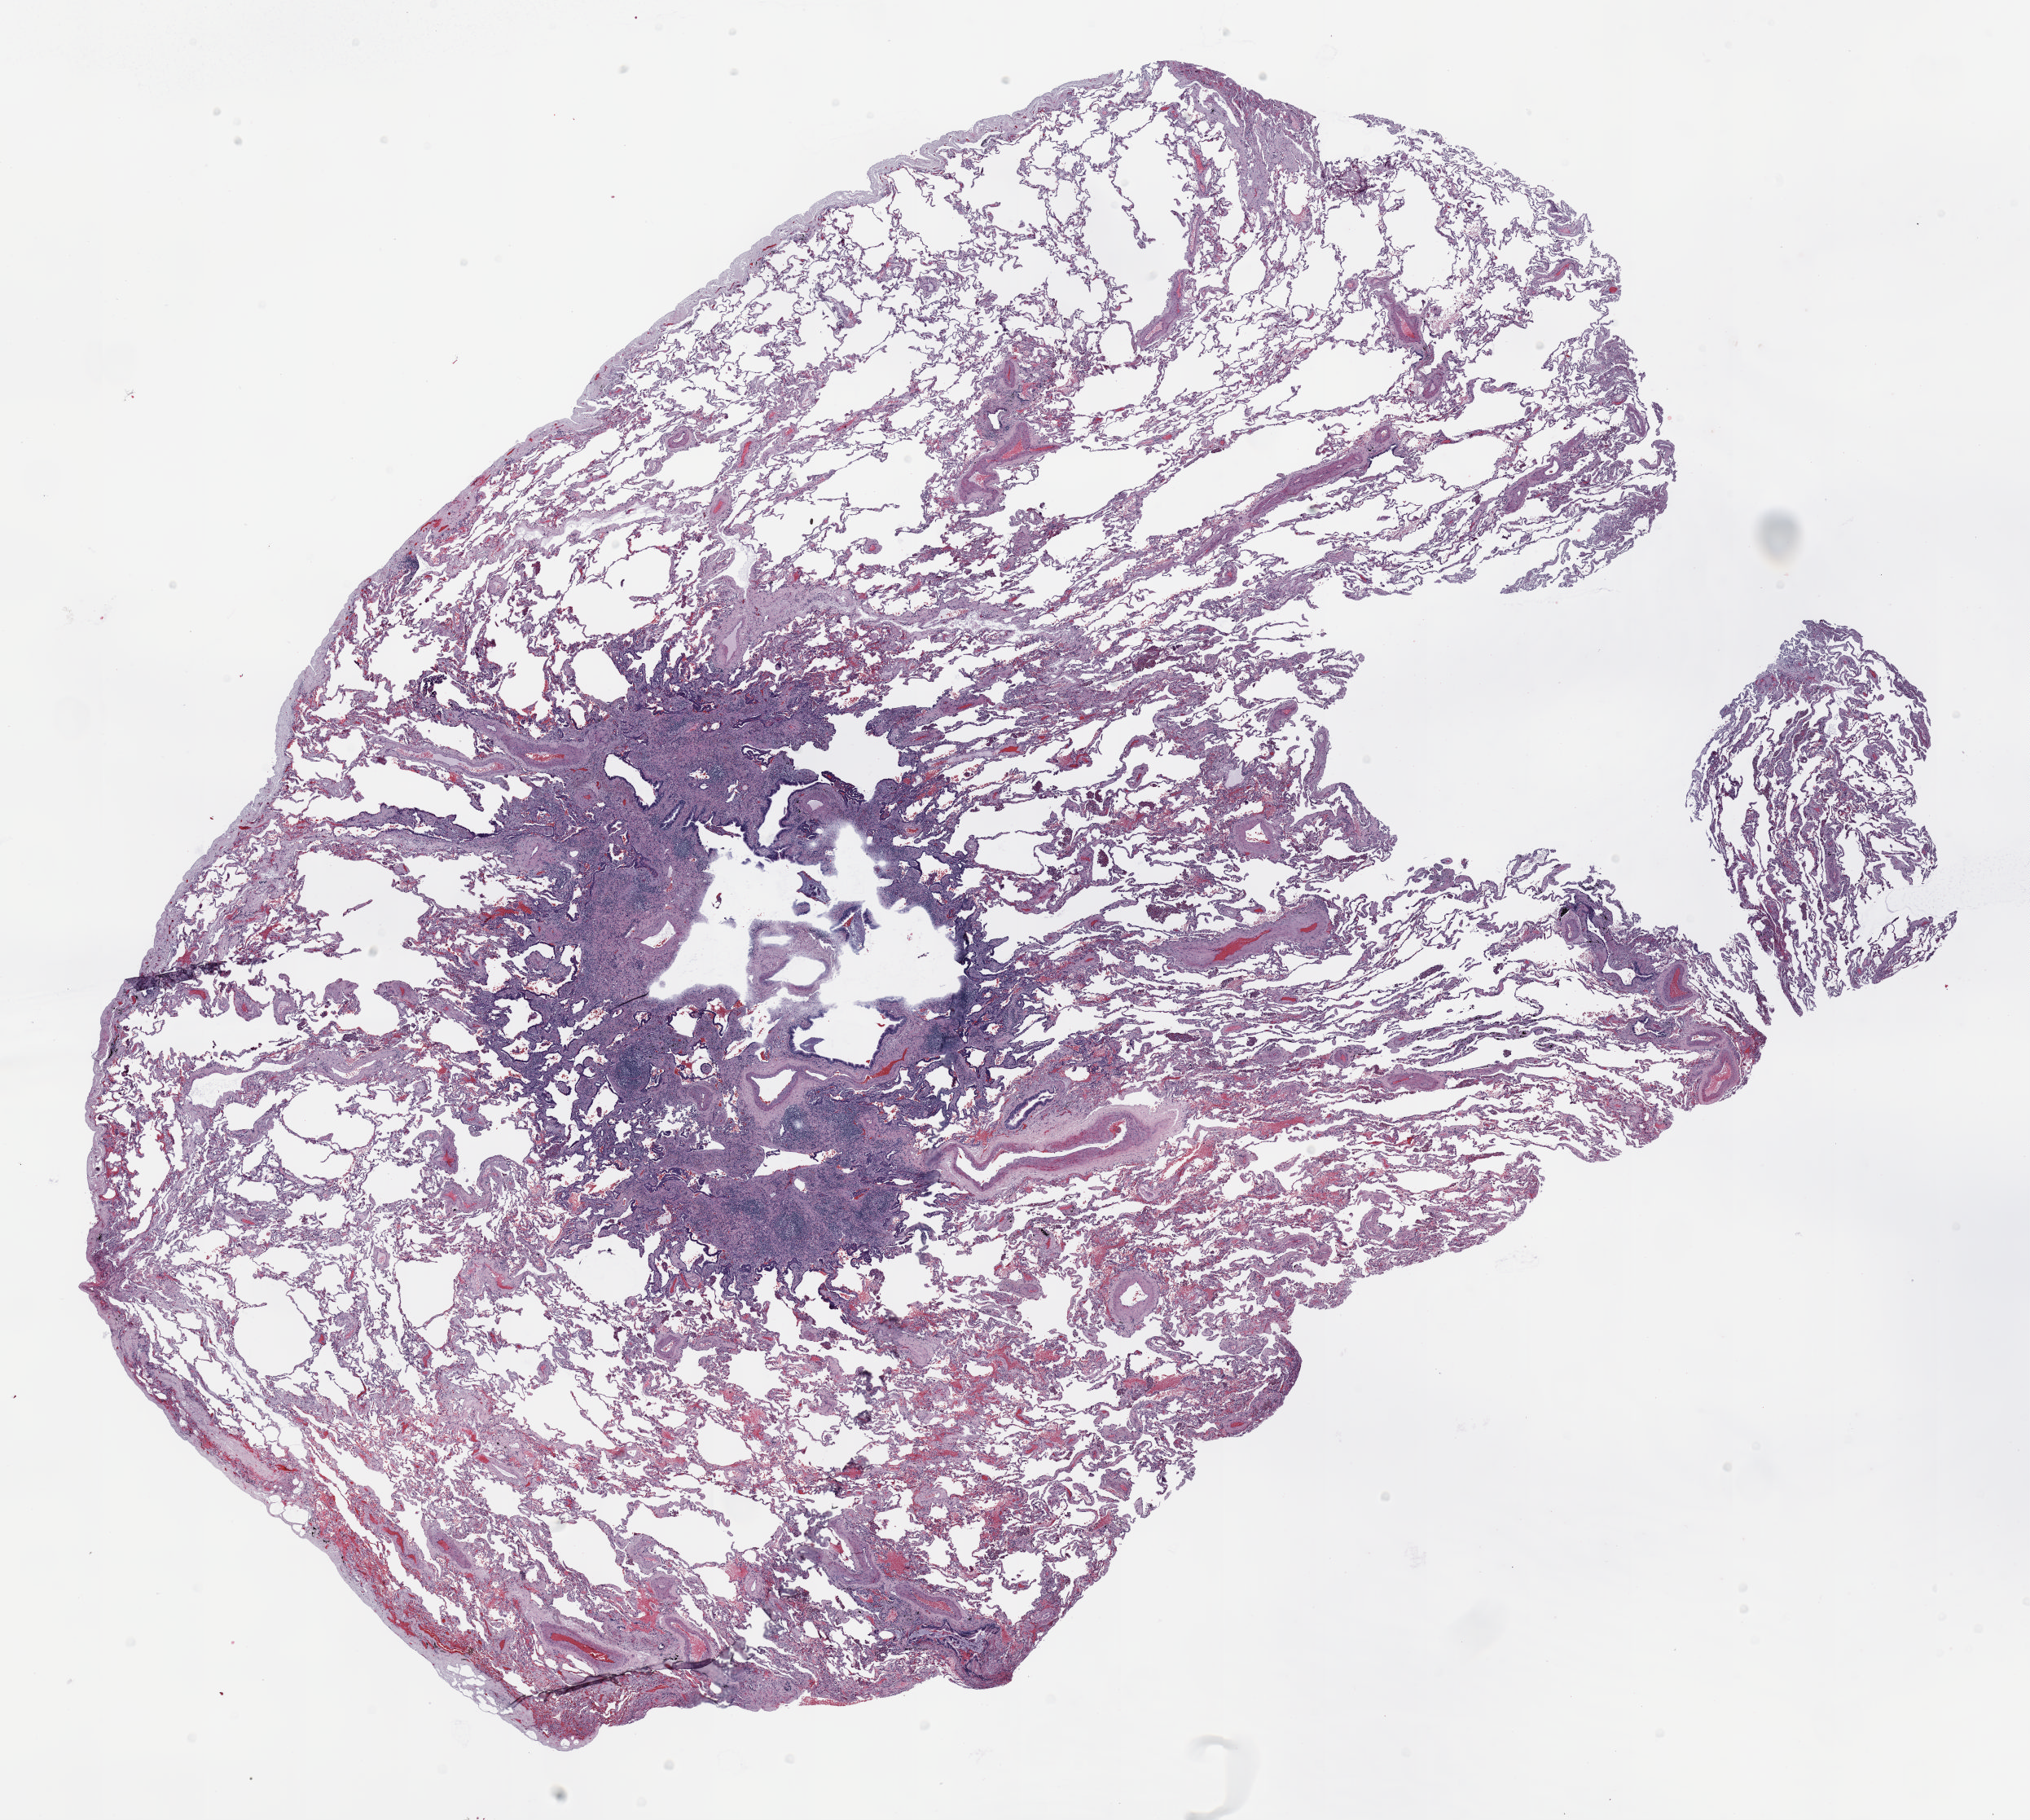
Whole-slide histology image, Hematoxylin and eosin (H&E) stained, whole scanned area (about 20.0 x 17.9 mm, slide scanned at 20x) shown as a low-resolution overview. Formalin-fixed paraffin-embedded (FFPE) section. Lung. Female, age 60 at enrolment. Current smoker at enrolment. Grade: well differentiated (G1).
Participant's lung-cancer diagnosis: Bronchiolo-alveolar adenocarcinoma, NOS (ICD-O-3 8250/3). Stage (AJCC 6th edition): IA. Tumour size (pathology): 11 mm. Primary tumour location (clinical record): right upper lobe.